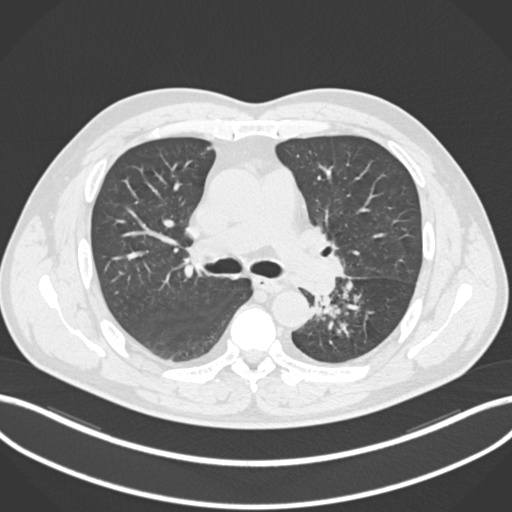
Chest CT, one axial slice; slice 140 of 223 in the series (ordered by position); reconstruction kernel B30f; 120 kVp; lung window (W 1500 / L -600 HU); 512 × 512 image matrix. Patient: male, 50 years. From the clinical record (not read from this slice): clinical TNM (as recorded): T2a N3 M0.
Annotated regions visible in this slice (bounding box drawn by a radiologist):
- lung tumour (recorded histology: squamous cell carcinoma): box from (x=308, y=274) to (x=339, y=303) px